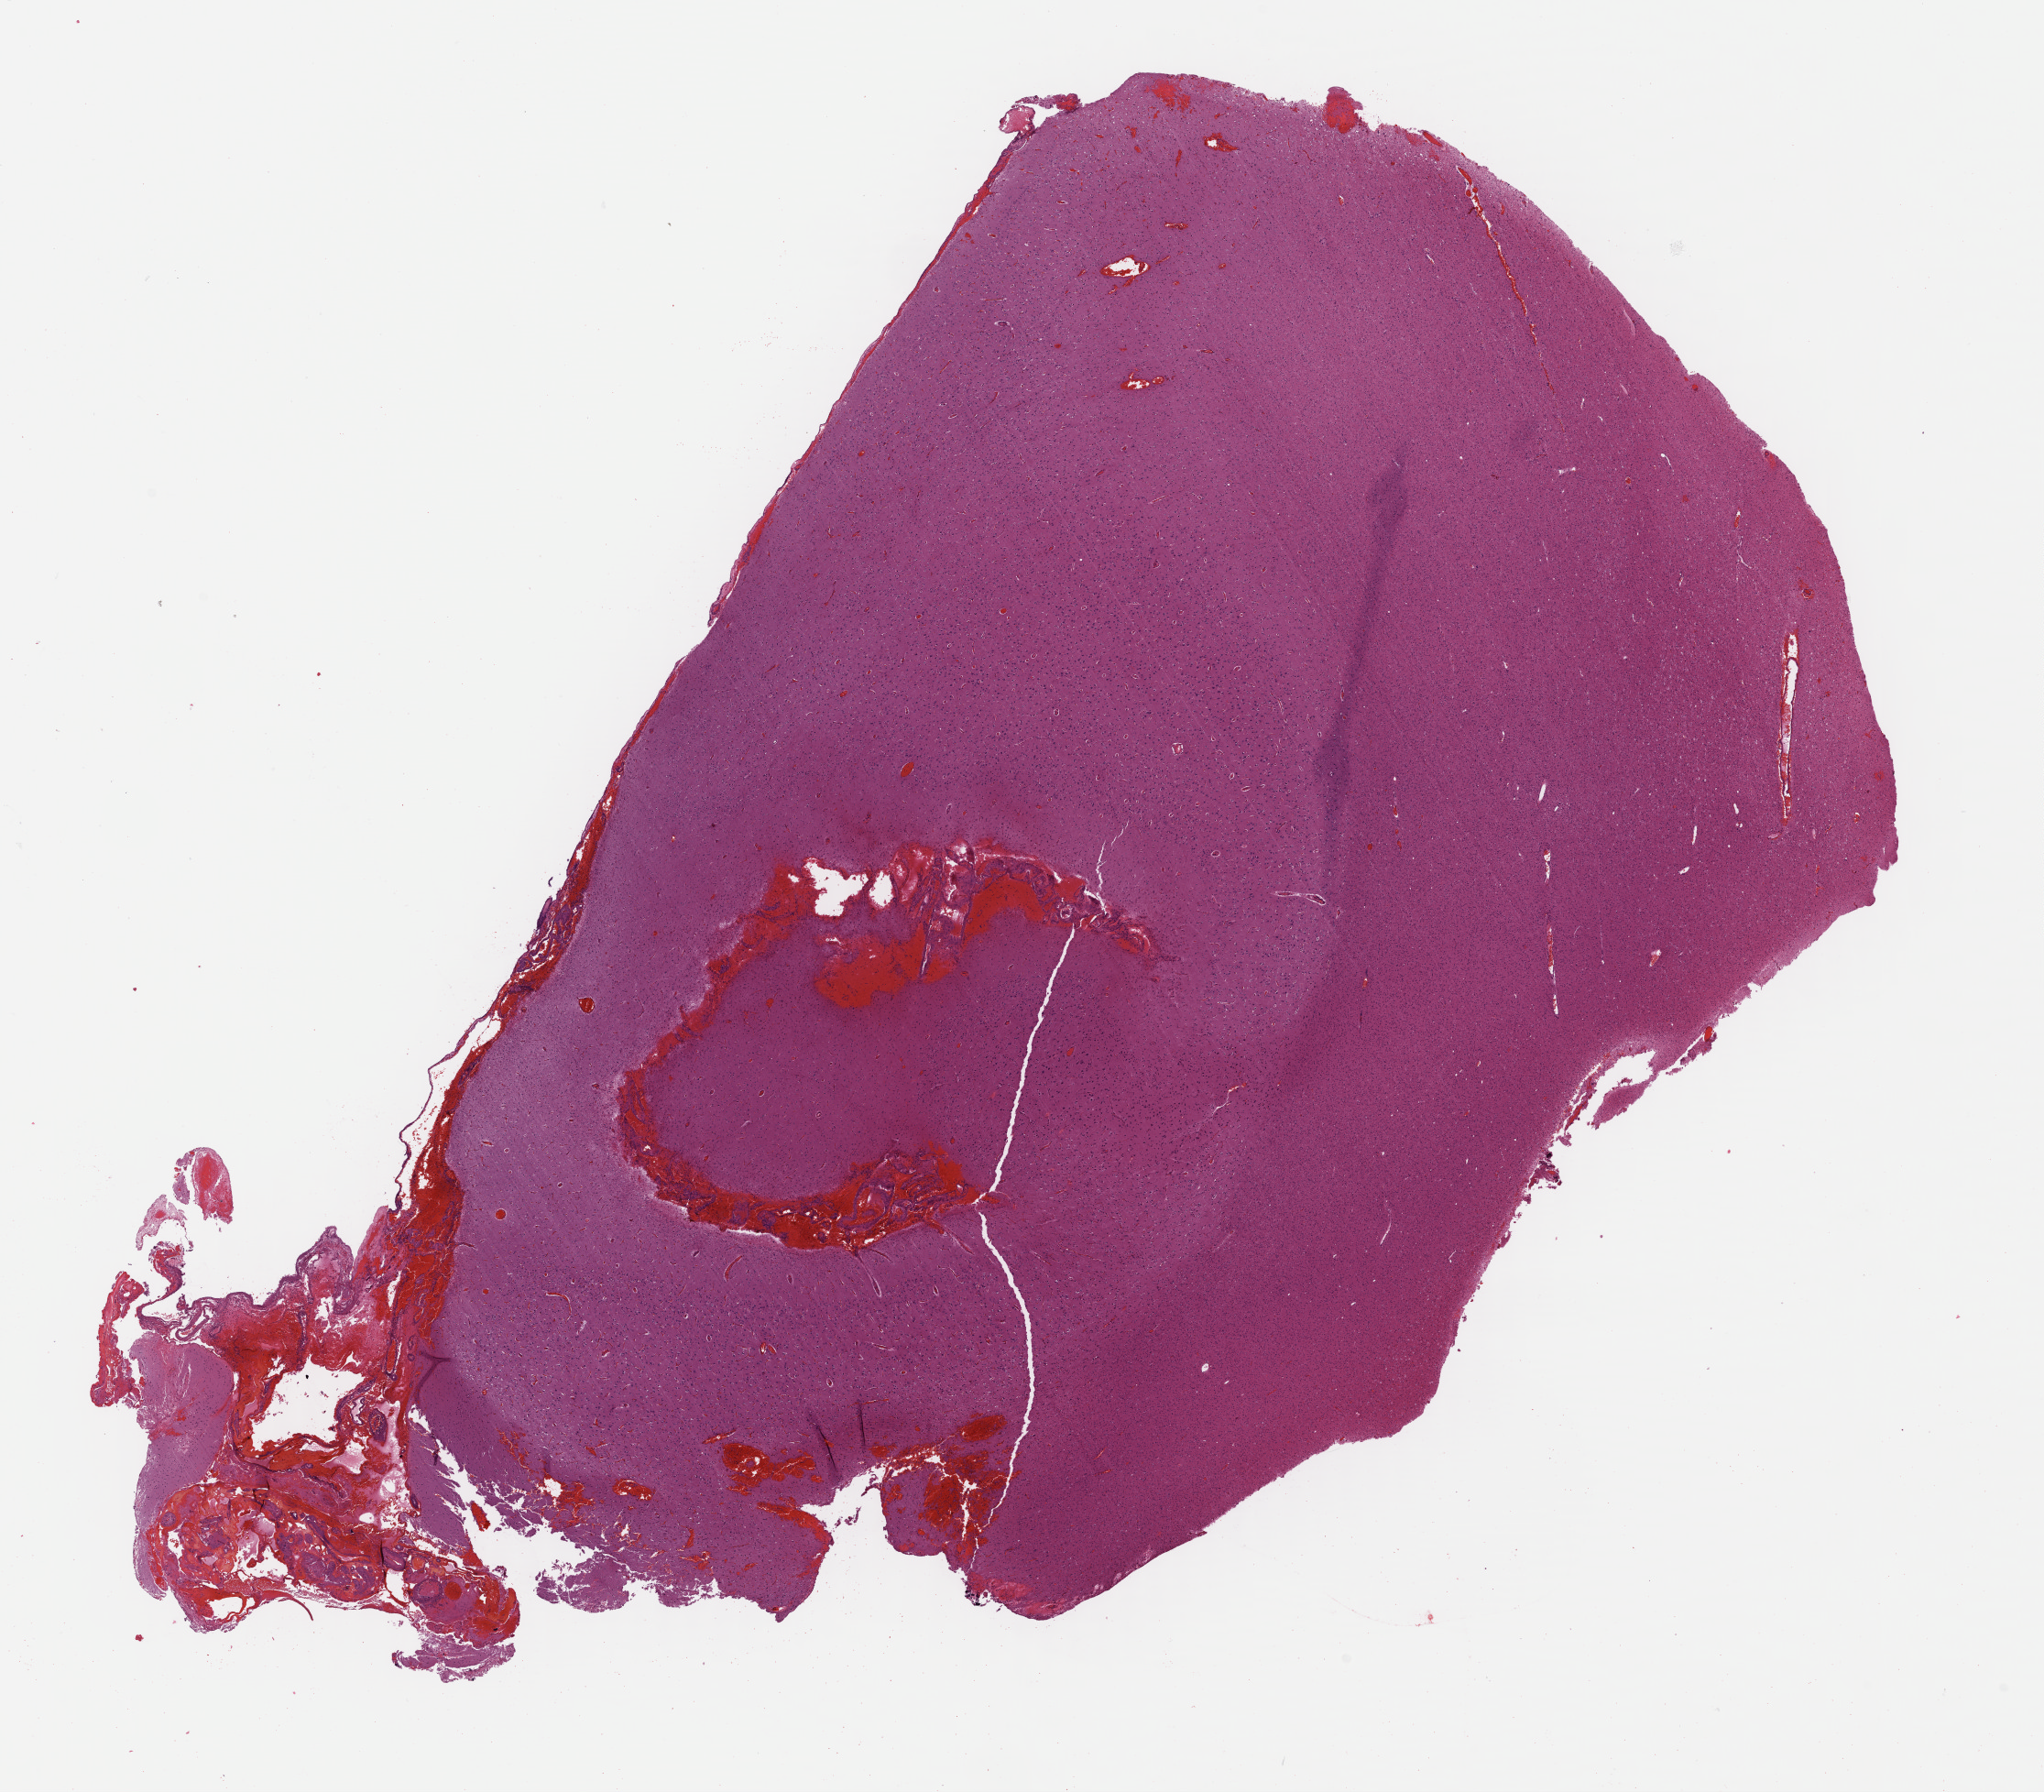
H&E whole-slide image — whole scanned area (about 17.5 x 15.4 mm, from a 40x scan) shown as a low-resolution overview, formalin-fixed paraffin-embedded (FFPE) diagnostic section, brain, primary tumour sample. Female patient; age at initial diagnosis 61 years. Histologic grade: G2 (moderately differentiated).
Histologic diagnosis: Astrocytoma, NOS. Laterality: left.